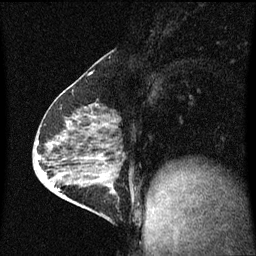
Breast MRI (dynamic contrast-enhanced), one sagittal slice; slice 27 of 60 in the series (ordered by position); dynamic contrast-enhanced series, image 2 of 3 at this slice position (ordered by acquisition); 1.5 T; TE 4.2 ms, TR 8 ms; 2 mm slice thickness; 256 × 256 image matrix, field of view 200 × 200 mm. Patient: female, 64 years.
Outlined on this slice (semi-automatic segmentation, software-assisted and operator-edited):
- analysis volume of interest (the breast-tissue region the enhancement analysis was run in; not a lesion): bounding box [x1, y1, x2, y2] px = [87, 176, 120, 217]
- tumour enhancement mask (voxels above the 70 % enhancement threshold inside the analysis volume of interest): [102, 180, 116, 195]